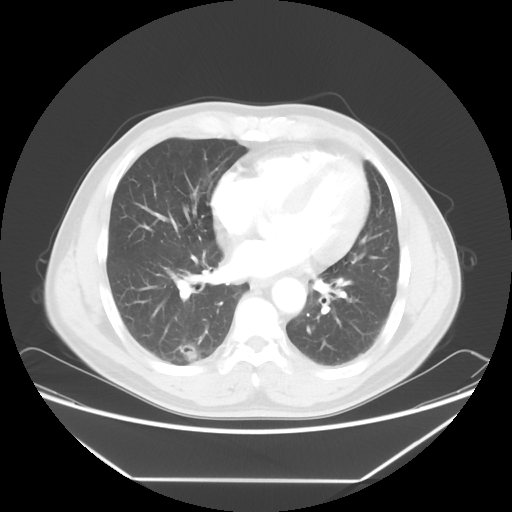
Chest CT, one axial slice. Position 29 of 65 along the scan axis. Reconstruction kernel STANDARD. Lung window (W 1500 / L -600 HU). 5 mm slice thickness. 512 × 512 image matrix. Patient: male, 50 years. From the clinical record (not read from this slice): clinical TNM (as recorded): T1c N0 M0; histopathological grade: G3.
Structures marked on this image (bounding box drawn by a radiologist):
- lung tumour (recorded histology: adenocarcinoma): bounding box [x1, y1, x2, y2] px = [174, 339, 207, 368]